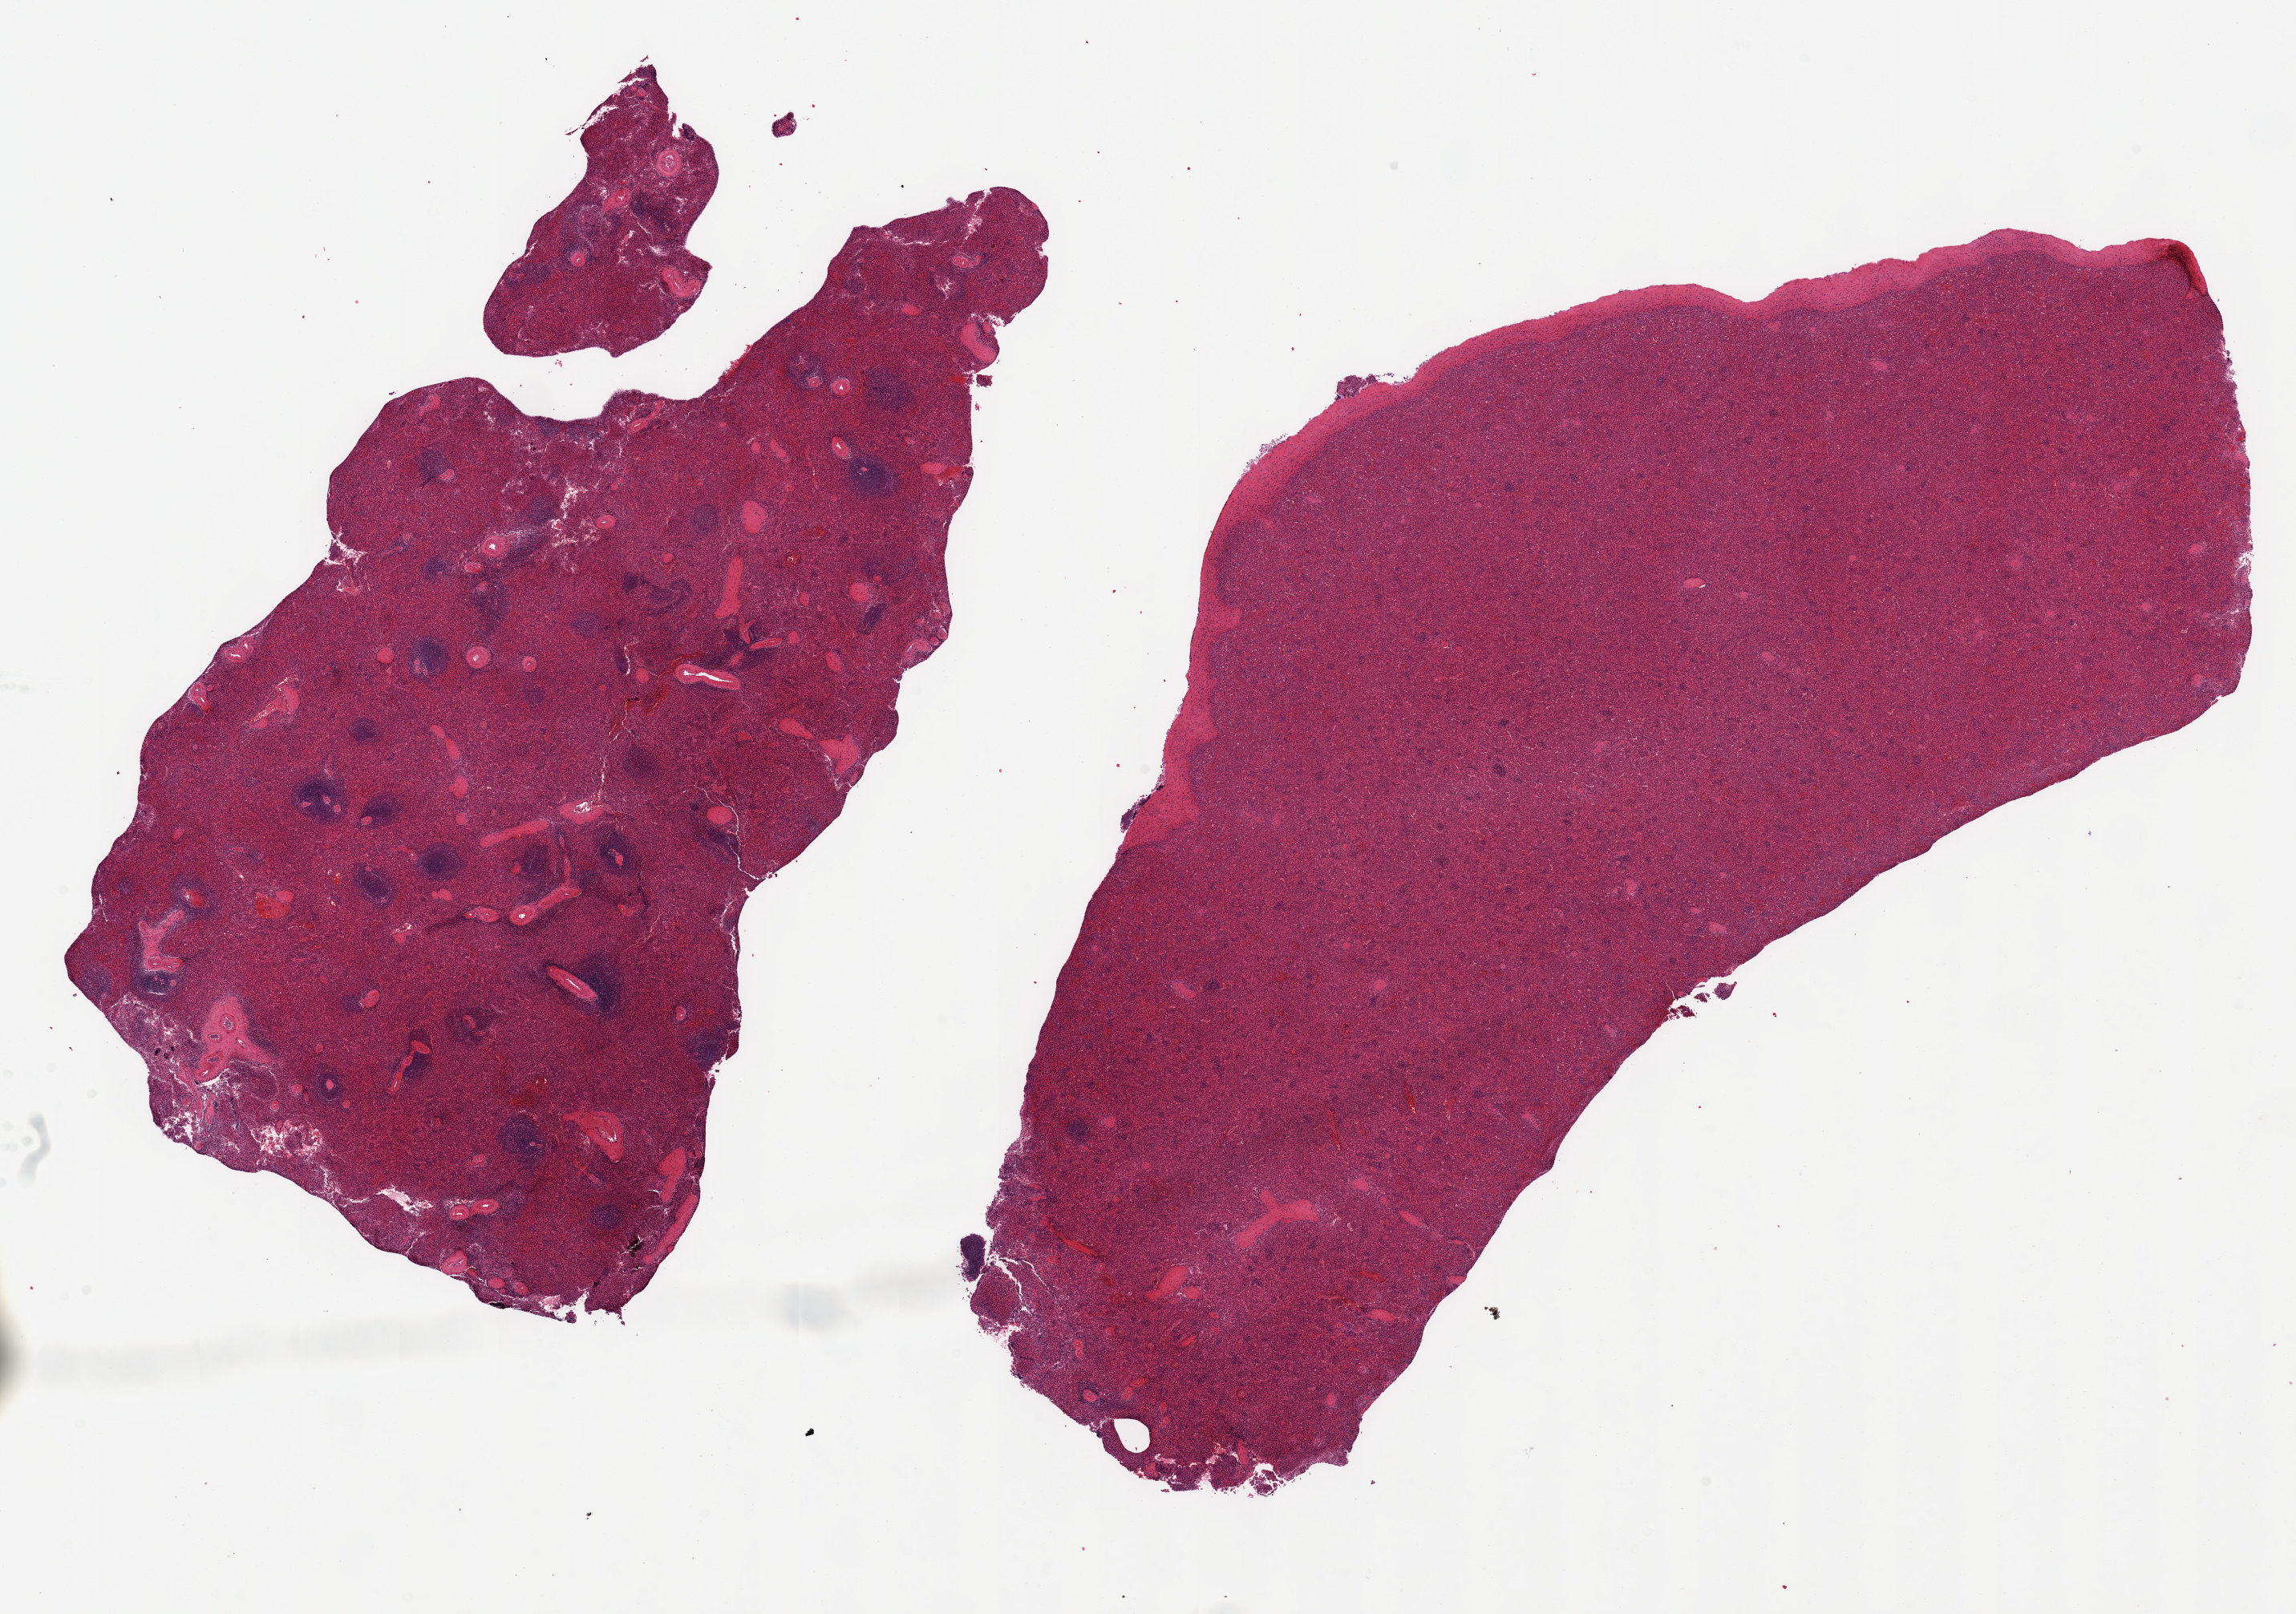
Digitized hematoxylin and eosin (H&E)-stained section, brightfield — low-resolution overview of the scanned area, about 22.6 x 15.9 mm (slide scanned at 20x); PAXgene-fixed paraffin-embedded (PFPE) section; target tissue: spleen; tissue donor sample. Male donor.
• reviewer comment on this tissue sample: 2 pieces; one piece includes portion of capsule (target is 5mm below capsule)